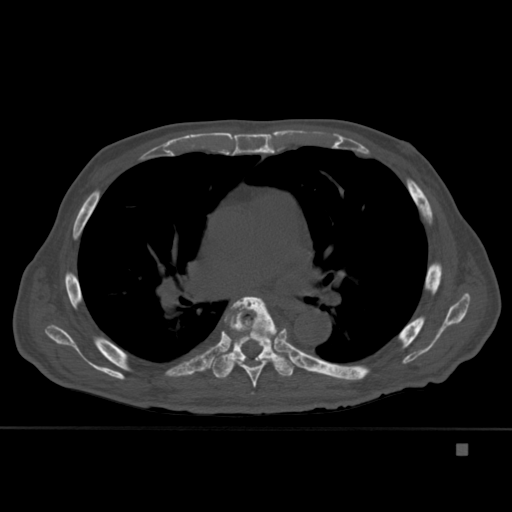
CT including the spine, one axial slice. Slice 287 of 451 in the series (ordered by position). Bone window (W 1800 / L 400 HU). 1.5 mm slice thickness. 512 × 512 image matrix, field of view 378 × 378 mm. Male patient, age 75 years. Case-level facts recorded for this patient, not image findings: primary cancer: prostate.
Outlined on this slice (semi-automatic segmentation, software-assisted and operator-edited):
- T5 vertebra: box from (x=251, y=392) to (x=254, y=394) px
- T6 vertebra: (x=224, y=296)–(x=278, y=388)
- T7 vertebra: (x=211, y=308)–(x=296, y=379)